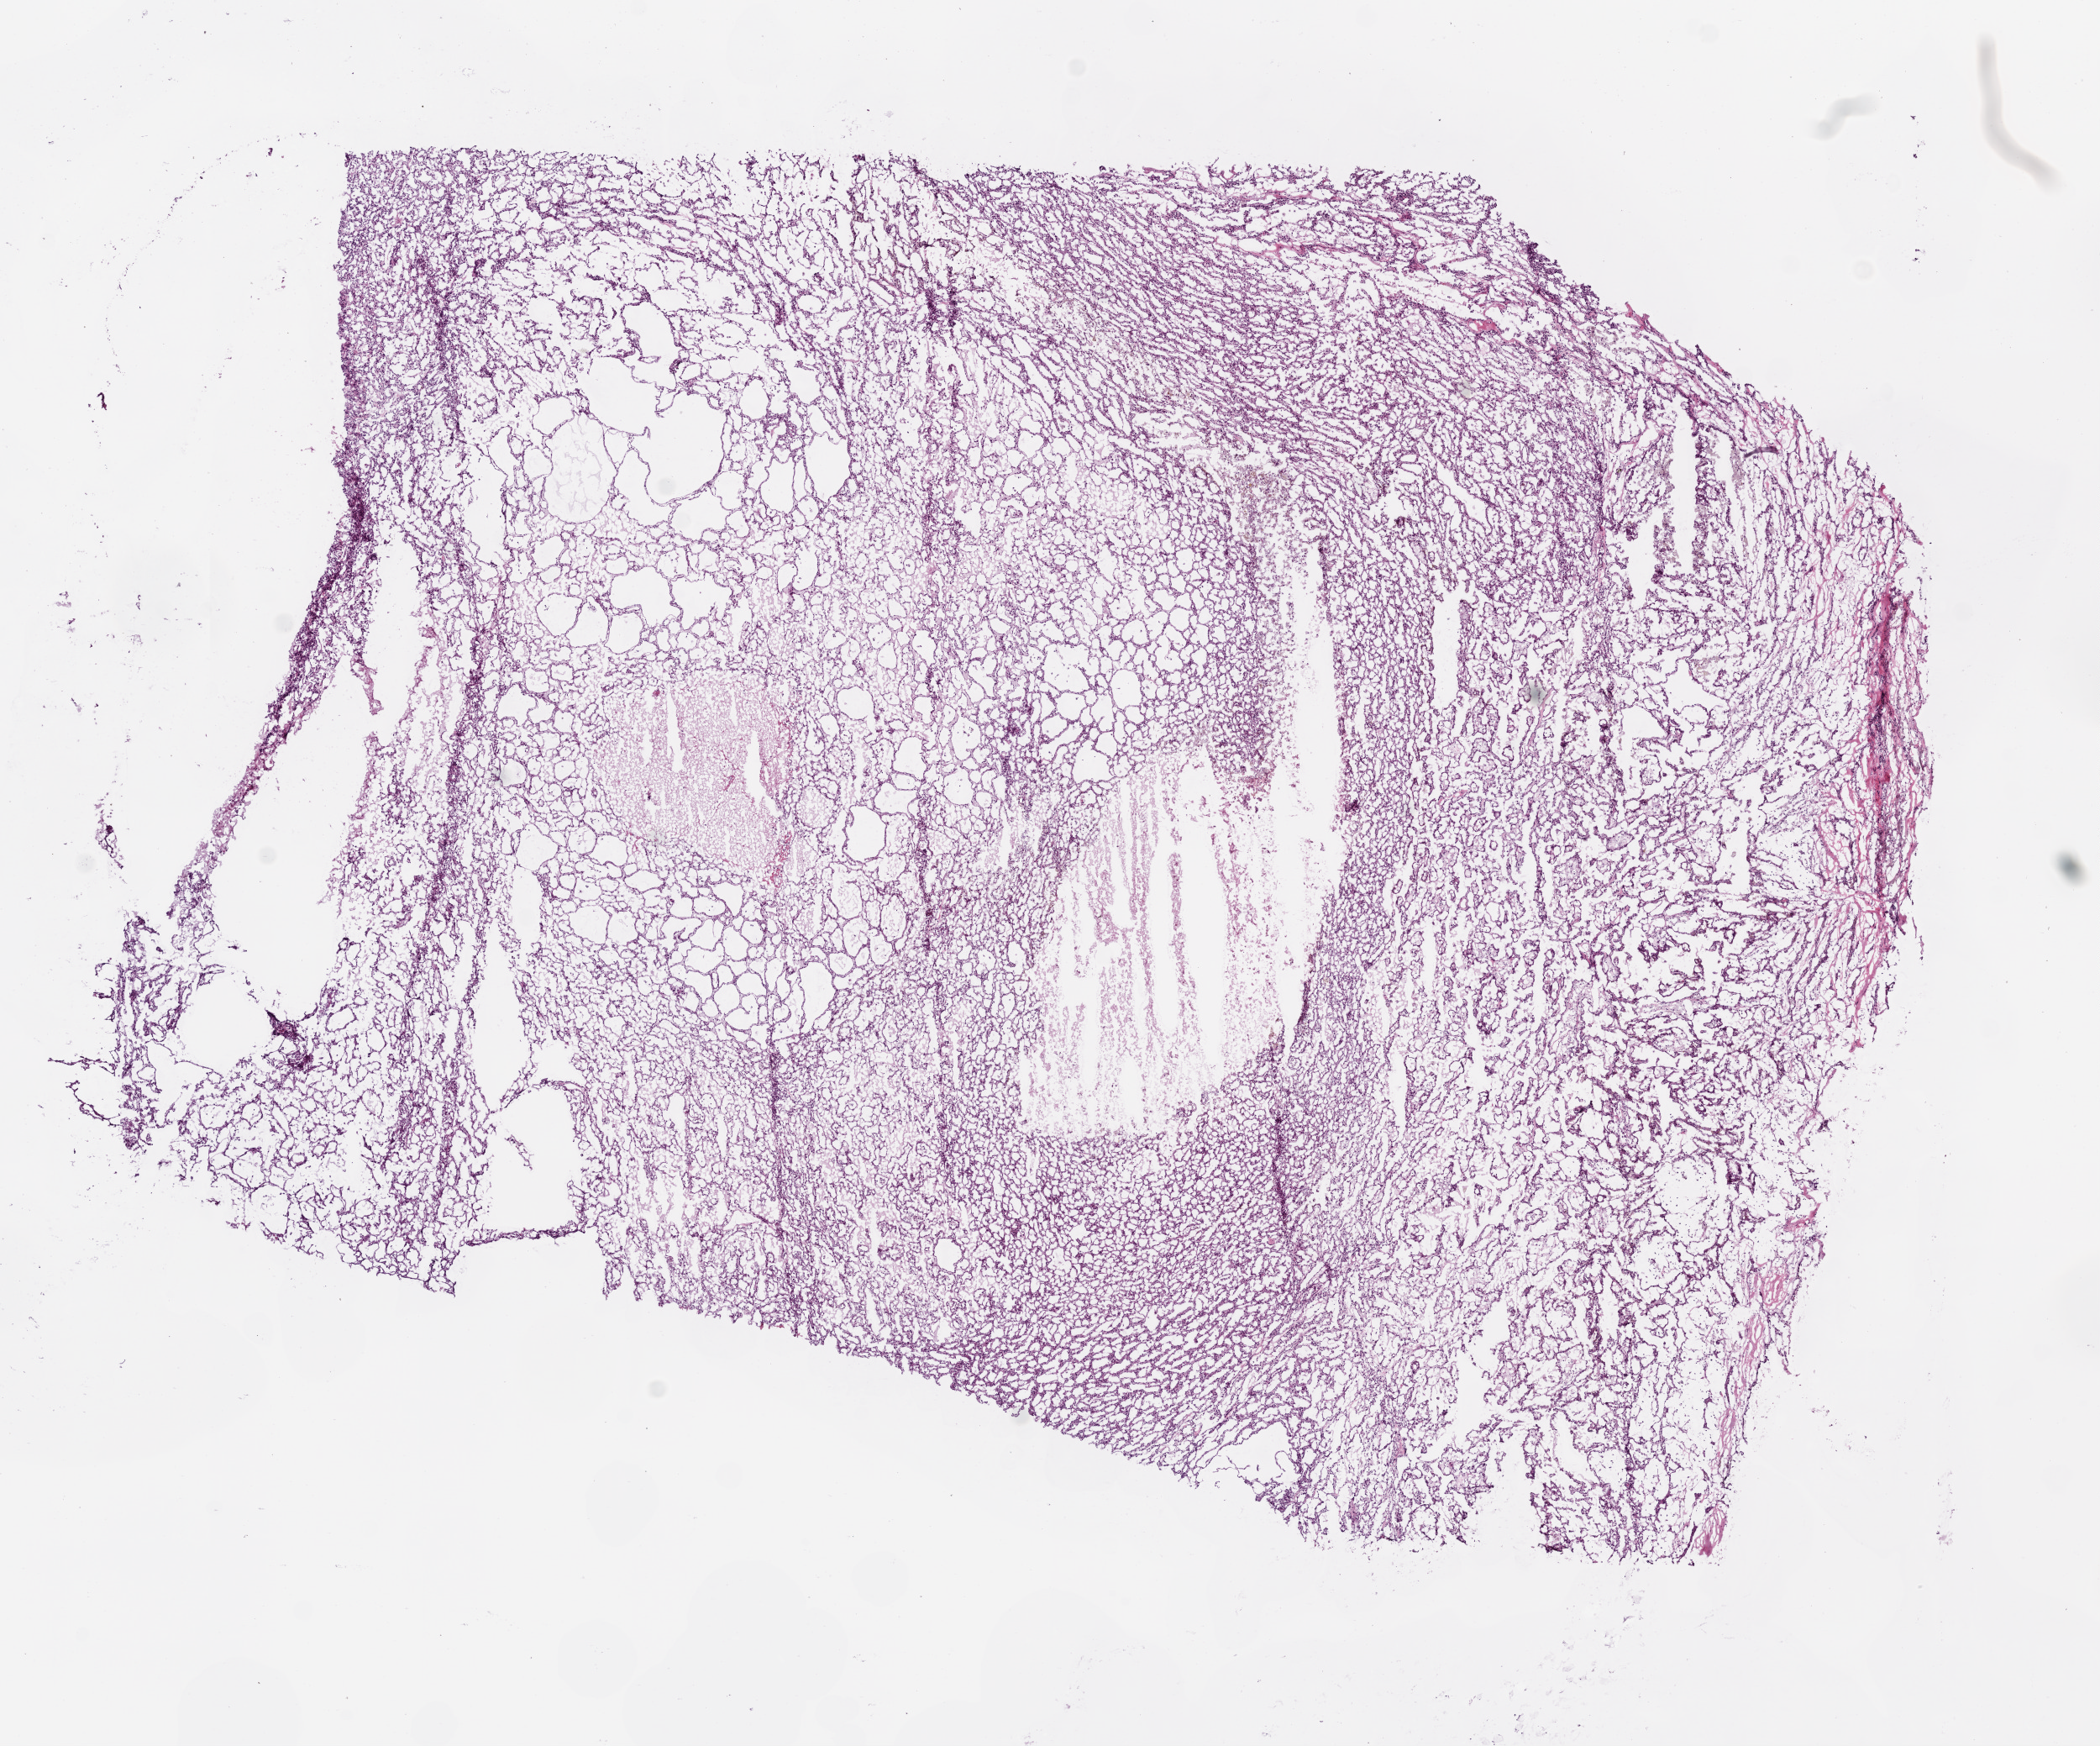
Whole-slide histology image, Hematoxylin and eosin (H&E) stained — low-resolution overview of the scanned area, about 10.0 x 8.3 mm (acquisition: 20x scan). Frozen section from the bottom of the tissue portion. Sample: primary tumour, kidney. Male, age 53 years at initial diagnosis. Slide review estimates, as recorded: tumour cells 90%, tumour nuclei 85%, normal cells 0%, stromal cells 10%, necrosis 0%.
Laterality: right. AJCC pathologic stage: I. TNM: T1a NX. Diagnosis: Papillary adenocarcinoma, NOS.